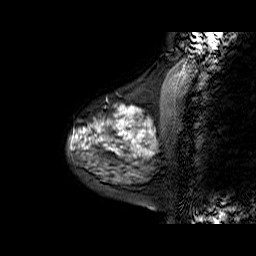
Breast MRI (dynamic contrast-enhanced), one sagittal slice. Slice 17 of 60 in the series (ordered by position). Dynamic contrast-enhanced series, time point 2 of 6 at this slice position (early post-contrast). 1.5 T. TE 6.3 ms, TR 32.9 ms. 256 × 256 image matrix. Female patient. From the clinical record (not read from this slice): setting: breast cancer imaged before/during neoadjuvant chemotherapy; receptor status: HR-positive, HER2-negative.
Structures marked on this image (semi-automatically segmented with operator editing):
- analysis volume of interest (the breast-tissue region the enhancement analysis was run in; not a lesion): bounding box (x1, y1, x2, y2) in pixels: (70, 86, 169, 170)
- tumour enhancement mask (voxels above the 100 % enhancement threshold inside the analysis volume of interest): (75, 106, 152, 155)